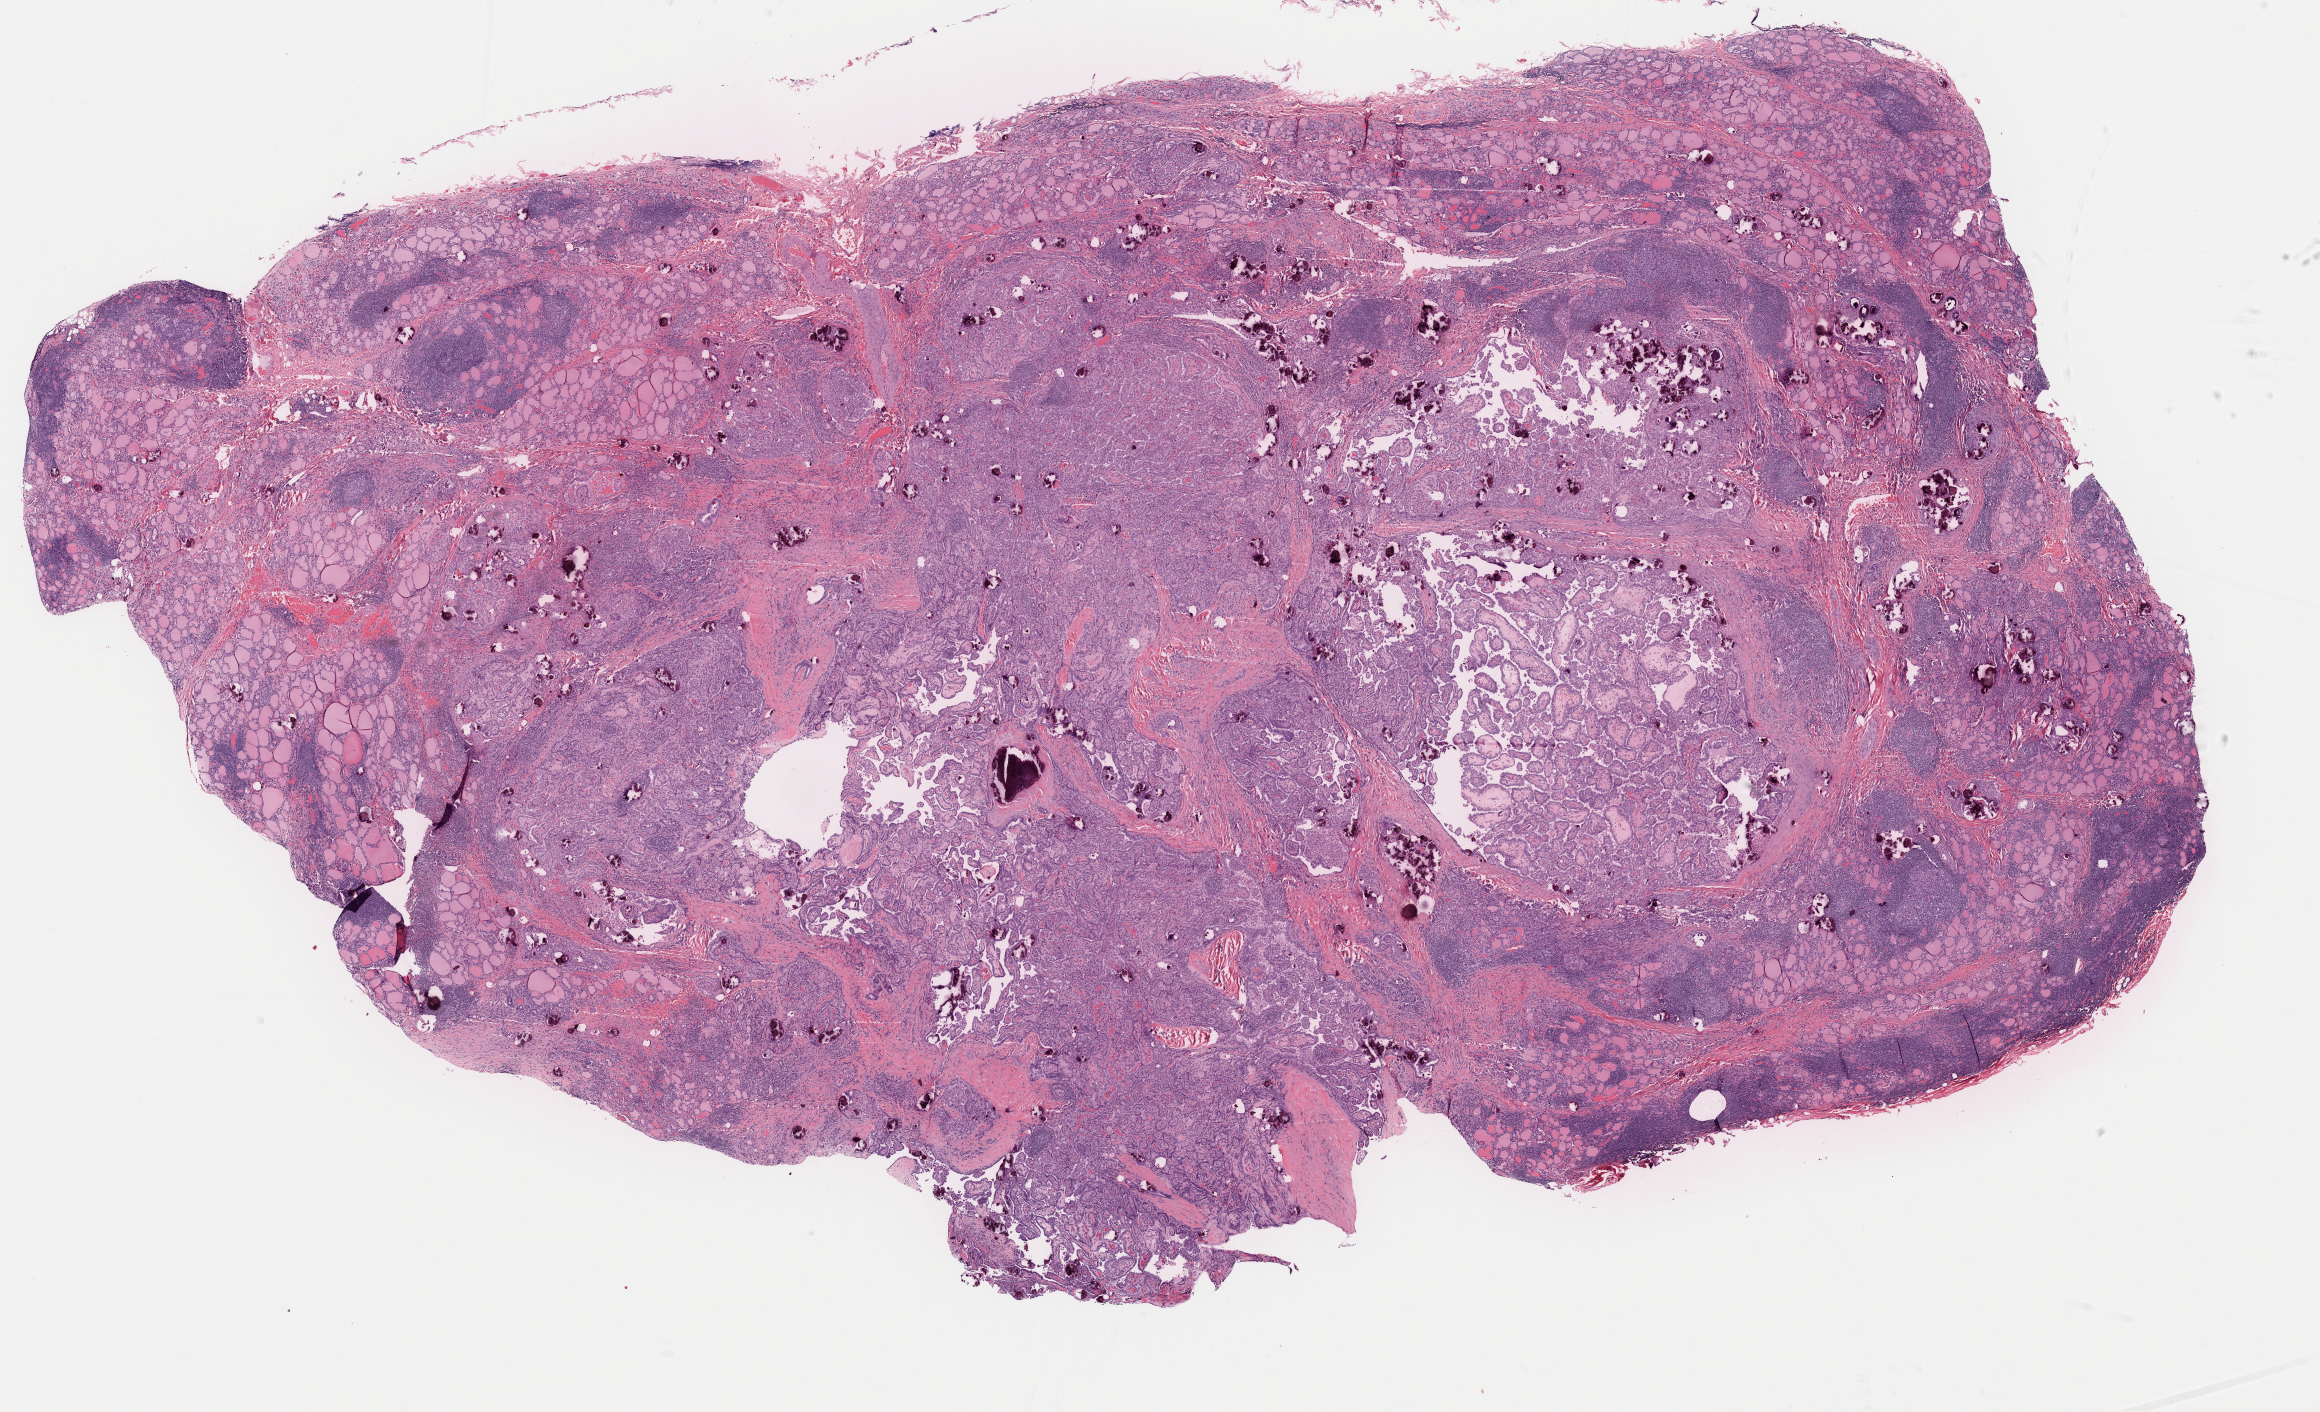
H&E-stained whole-slide image — a low-resolution overview of the entire scanned area, about 18.3 x 11.2 mm (acquisition: 40x scan); formalin-fixed paraffin-embedded (FFPE) diagnostic section; sample: primary tumour, thyroid. Patient: female, age at initial diagnosis 22 years.
Pathologic diagnosis: Papillary adenocarcinoma, NOS. AJCC pathologic stage: I.